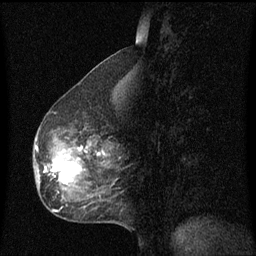
Breast MRI (dynamic contrast-enhanced), one sagittal slice. Position 29 of 60 along the scan axis. Dynamic contrast-enhanced series, image 2 of 3 at this slice position (ordered by acquisition). 1.5 T. TE 4.2 ms, TR 8.4 ms. 256 × 256 image matrix. Female patient, age 49 years. From the clinical record (not read from this slice): setting: breast cancer imaged before/during neoadjuvant chemotherapy; receptor status: HR-positive, HER2-negative.
Annotated regions visible in this slice (semi-automatic segmentation, software-assisted and operator-edited):
- analysis volume of interest (the breast-tissue region the enhancement analysis was run in; not a lesion): bounding box (x1, y1, x2, y2) in pixels: (34, 128, 115, 201)
- tumour enhancement mask (voxels above the 70 % enhancement threshold inside the analysis volume of interest): (47, 146, 89, 185)